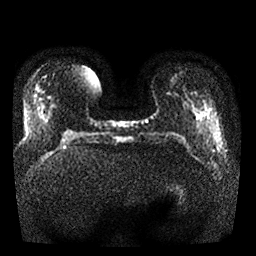
Breast MRI, one axial slice. Position 5 of 25 along the scan axis. Diffusion-weighted series; image 2 of 4 stored at this slice position (different b-values; order by instance number). 1.5 T. 4 mm slice thickness. 256 × 256 image matrix, field of view 340 × 340 mm. Female patient.
Structures marked on this image (manually delineated by an expert):
- tumour on diffusion-weighted imaging: bounding box [x1, y1, x2, y2] px = [197, 116, 201, 119]